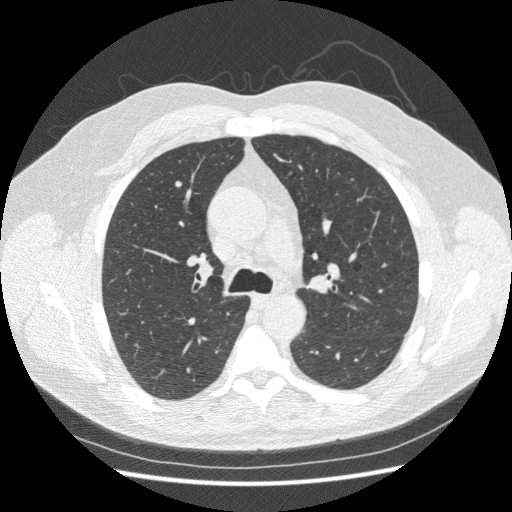
Chest CT (low-dose screening protocol), one axial image; first (baseline) screen; lung window (W 1500 / L -600 HU); 1.25 mm slice thickness; slice 92 of 250 in the series; 512 × 512 image matrix. Male, age 63 years at enrolment. Current smoker at enrolment.
• Expert reader's lesion annotation, box from (x=167, y=175) to (x=187, y=192) px.
• Reader record for this screening exam (exam-level; its link to the box is not recorded): non-calcified nodule or mass ≥4 mm, right upper lobe, 5 × 4 mm, smooth margins, soft tissue attenuation.
• Official screen result: positive, change unspecified: nodule(s) >= 4 mm or enlarging nodule(s), mass(es), or other non-specific abnormalities suspicious for lung cancer.
• Later outcome: lung cancer diagnosed 202 days after this screen — large cell carcinoma, NOS, right upper lobe, poorly differentiated (G3), stage IIIA (AJCC 6th edition), 15 mm at pathology.